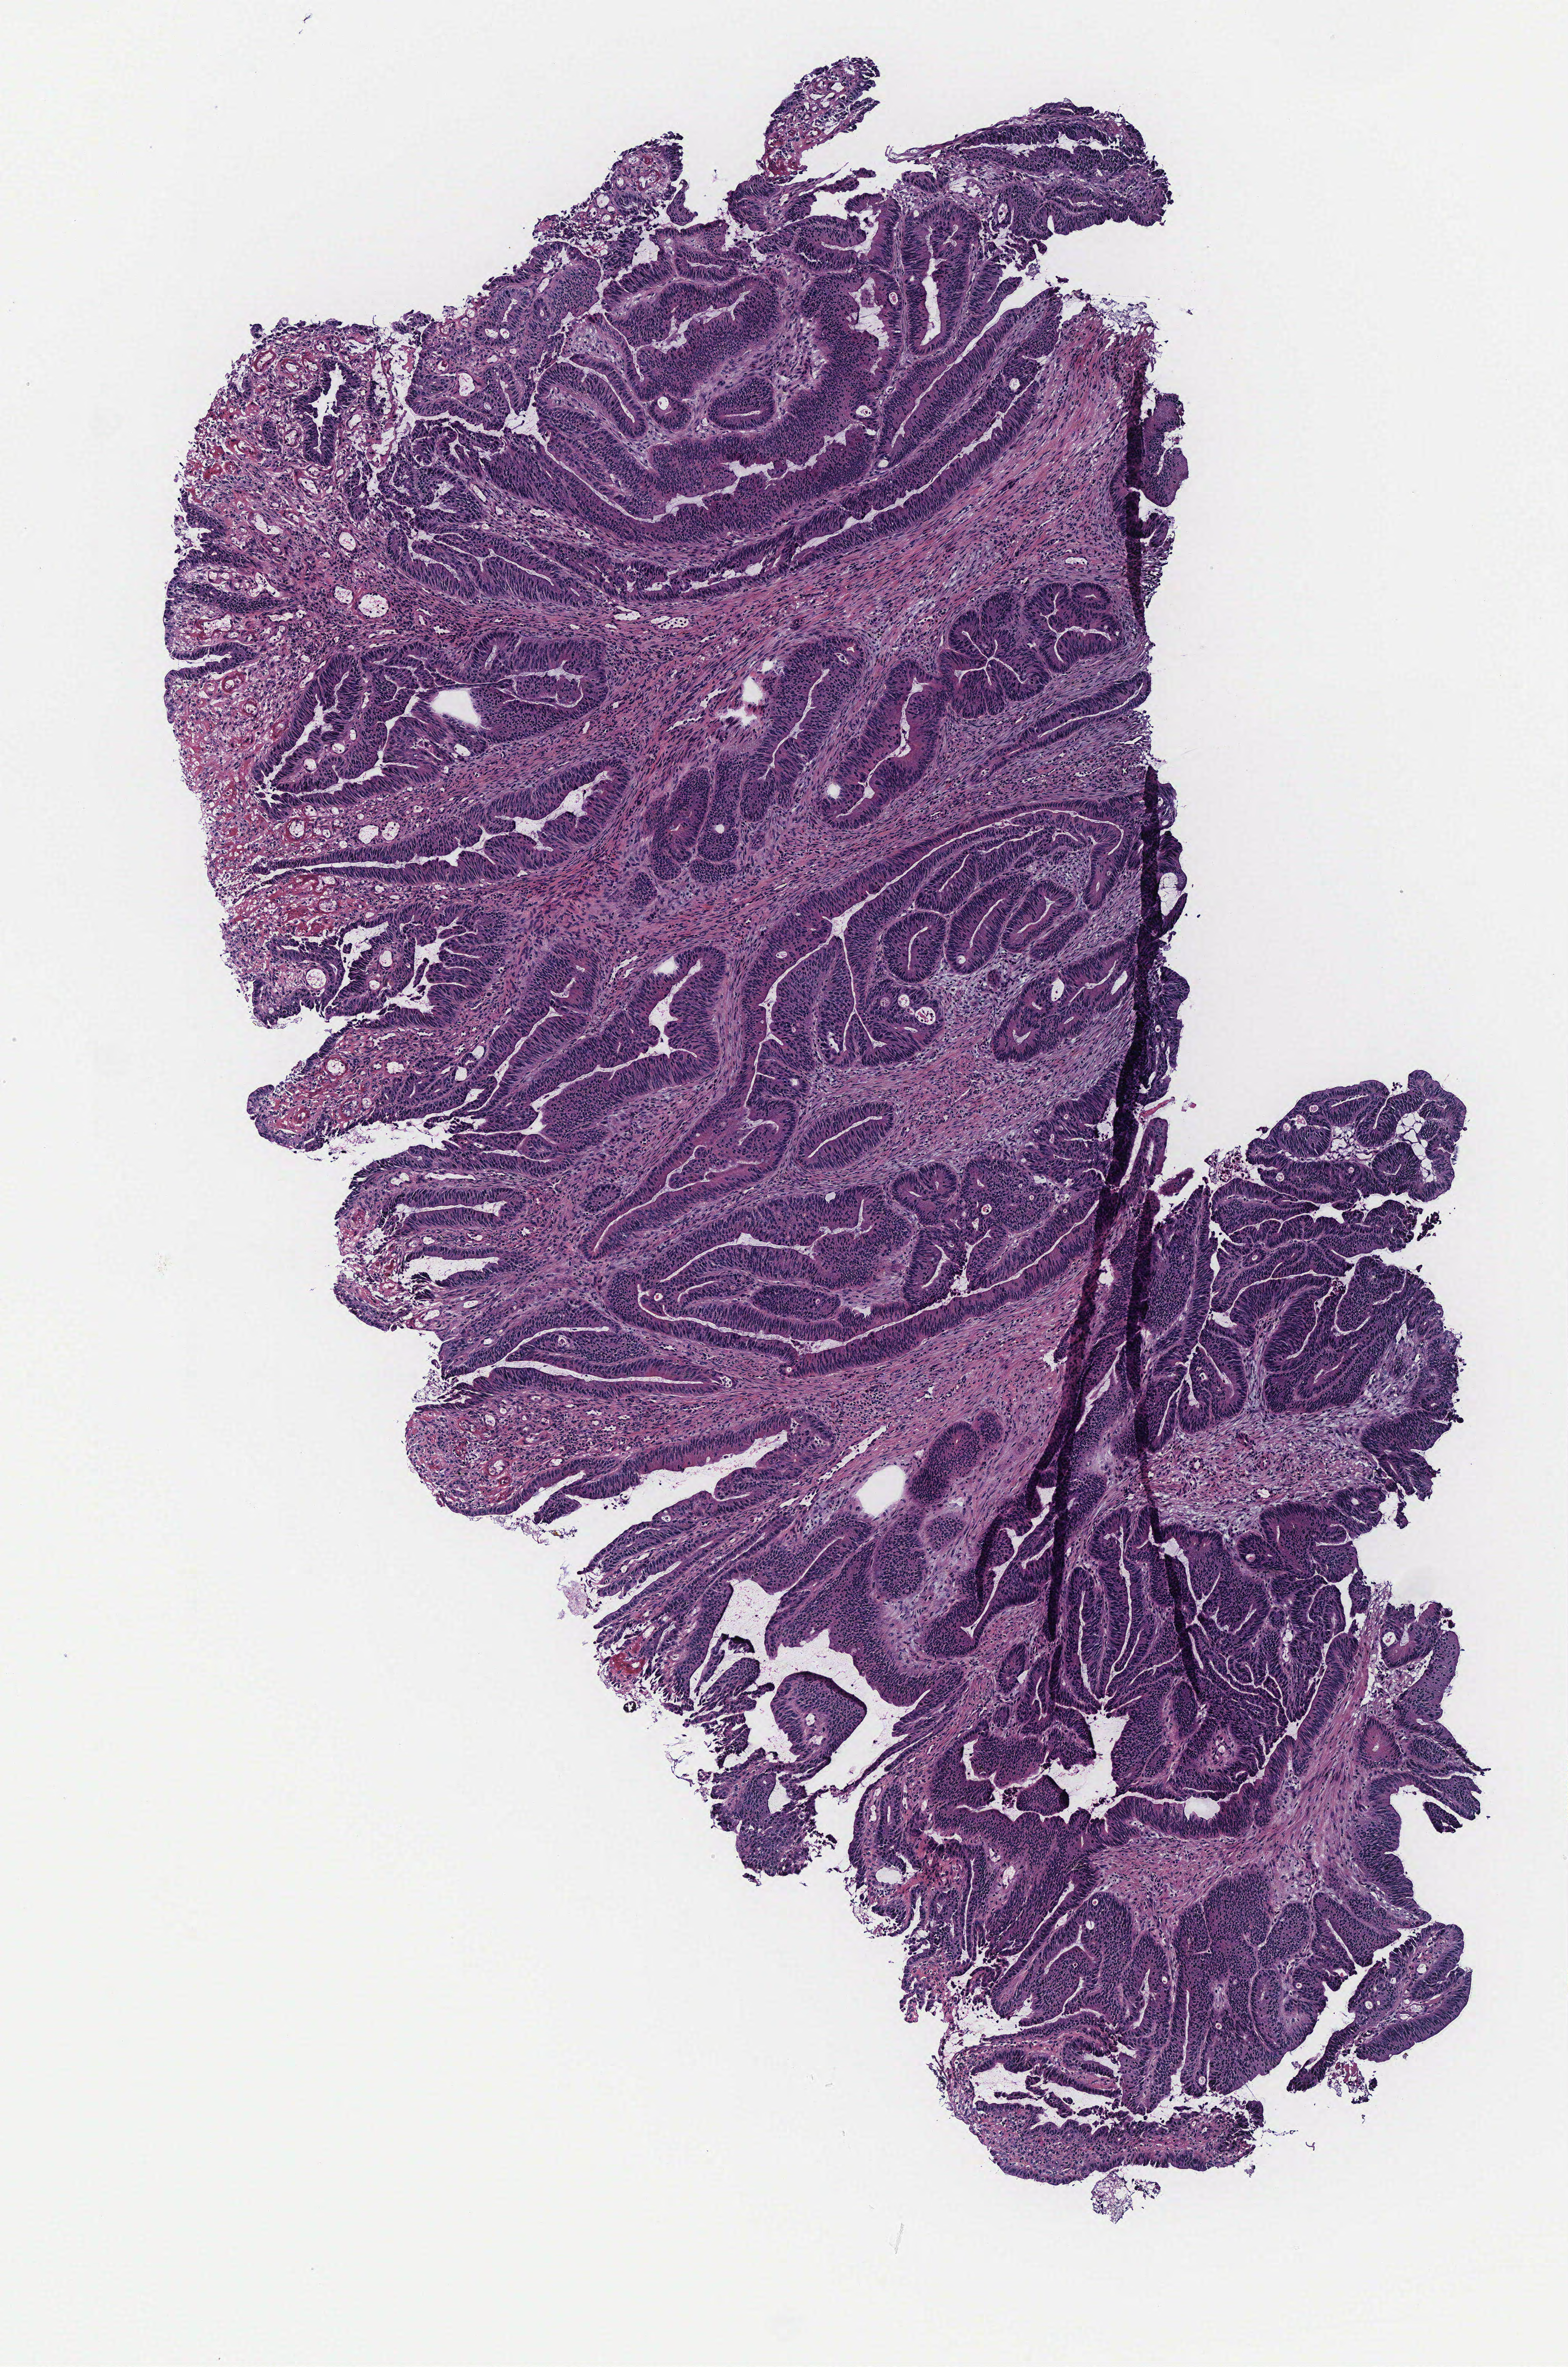
Hematoxylin and eosin (H&E) stained whole-slide image — shown as a low-resolution overview of the whole scanned area (about 4.1 x 6.2 mm); colon, tissue type not recorded. Patient sex: male.
Patient diagnosis: Adenocarcinoma, NOS.